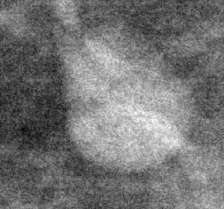
Cropped region of a digitized screen-film mammogram centred on a radiologist-marked abnormality, right breast, MLO view.
Mass, shape lymph node; BI-RADS assessment category 2; benign without callback (not worked up further).